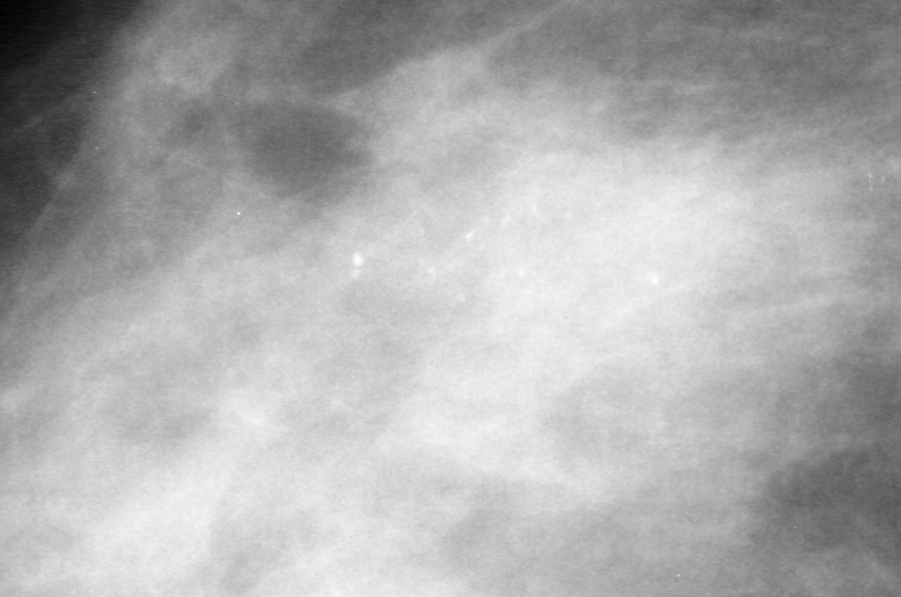
Cropped region of a digitized screen-film mammogram centred on a radiologist-marked abnormality, right breast, CC view.
Calcifications, morphology pleomorphic, distribution clustered; BI-RADS assessment category 0 (incomplete: needs additional imaging); subtlety rating 4 on a 1 (subtle) to 5 (obvious) scale; pathology (as recorded): malignant.